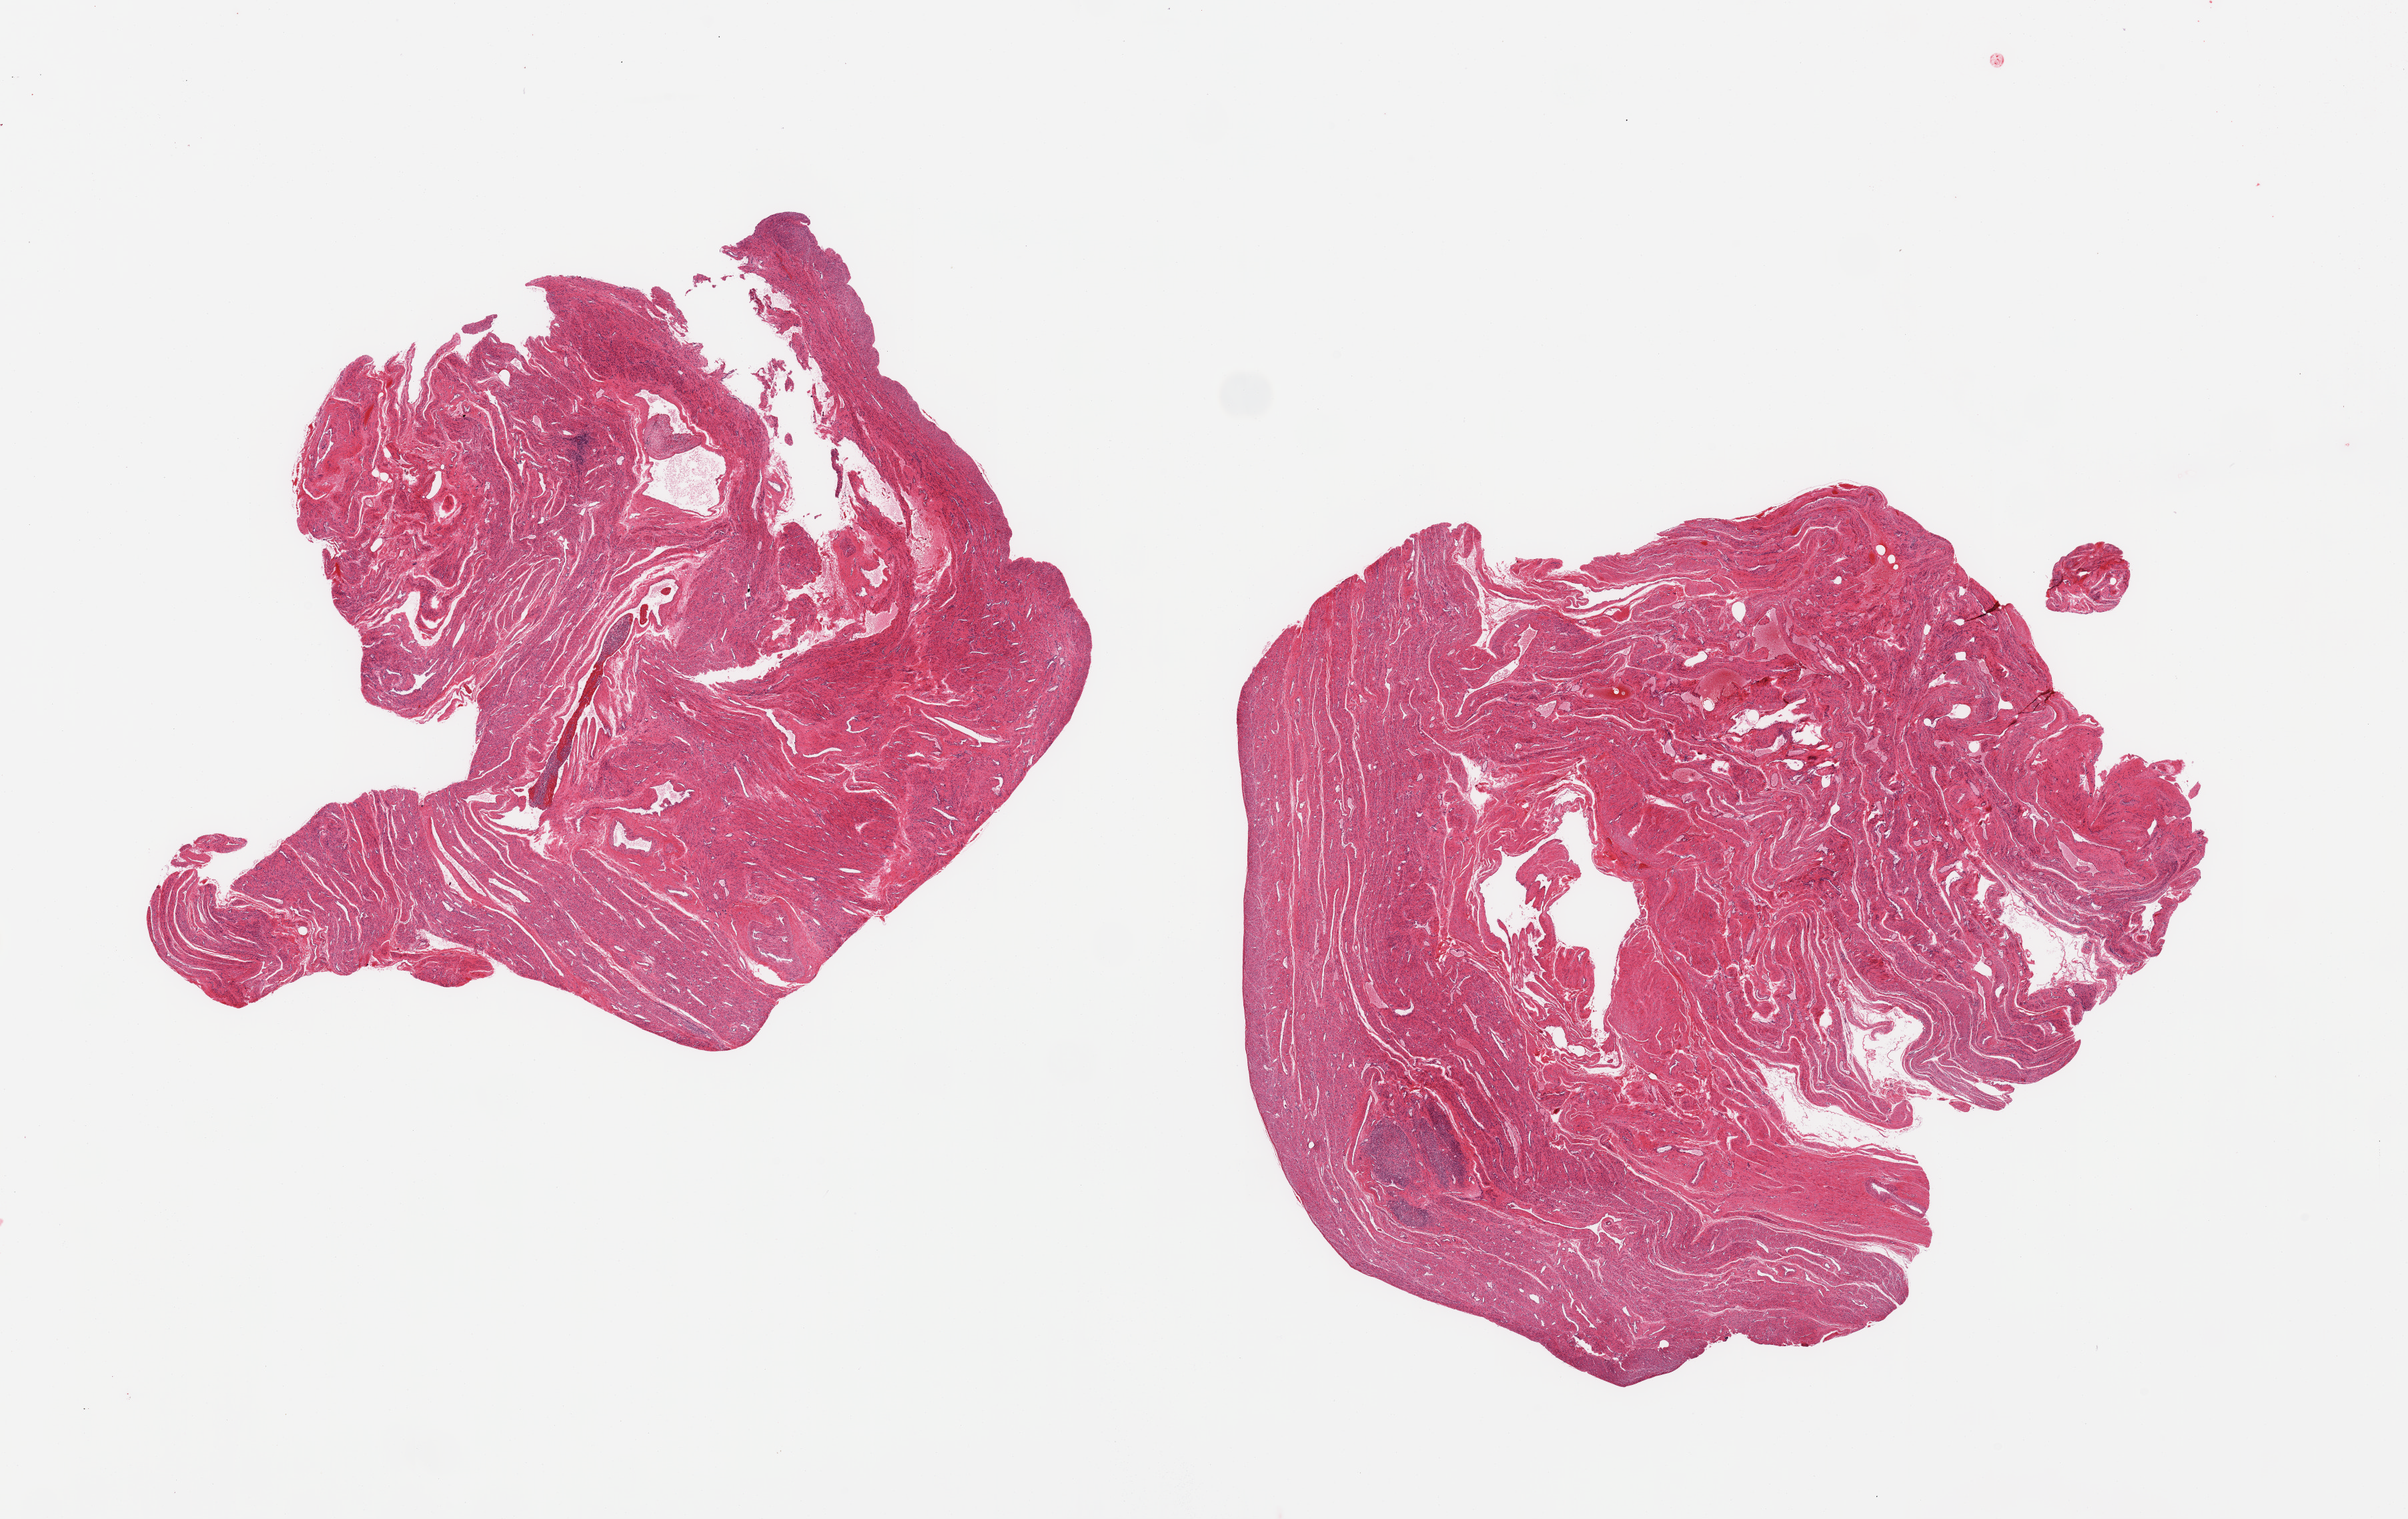
Whole-slide image, haematoxylin and eosin stain, brightfield — shown as a low-resolution overview of the whole scanned area (about 28.5 x 18.0 mm), PAXgene-fixed, paraffin-embedded tissue, section of uterus (target tissue), donor tissue sample.
Pathologist's review note for this sample: 2 pieces. myometrium.